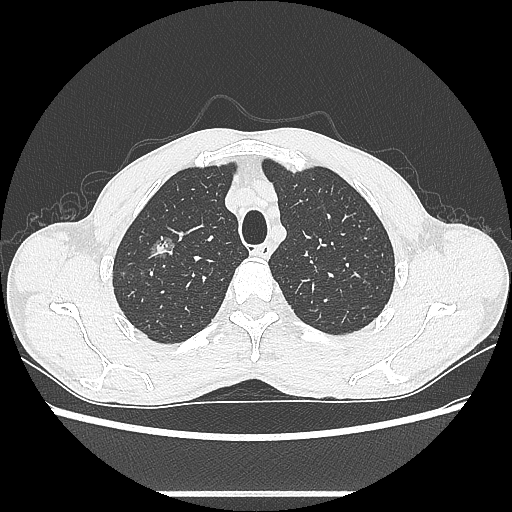
Chest CT, one axial slice; slice 486 of 601 in the series (ordered by position); reconstruction kernel LUNG; lung window (W 1500 / L -600 HU); 512 × 512 image matrix, field of view 357 × 357 mm. Patient: male, 54 years. Case-level facts recorded for this patient, not image findings: clinical TNM (as recorded): T1a N0 M0.
Structures marked on this image (bounding box drawn by a radiologist):
- lung tumour (recorded histology: adenocarcinoma): bounding box <144,232,181,268> (left, top, right, bottom; pixels)